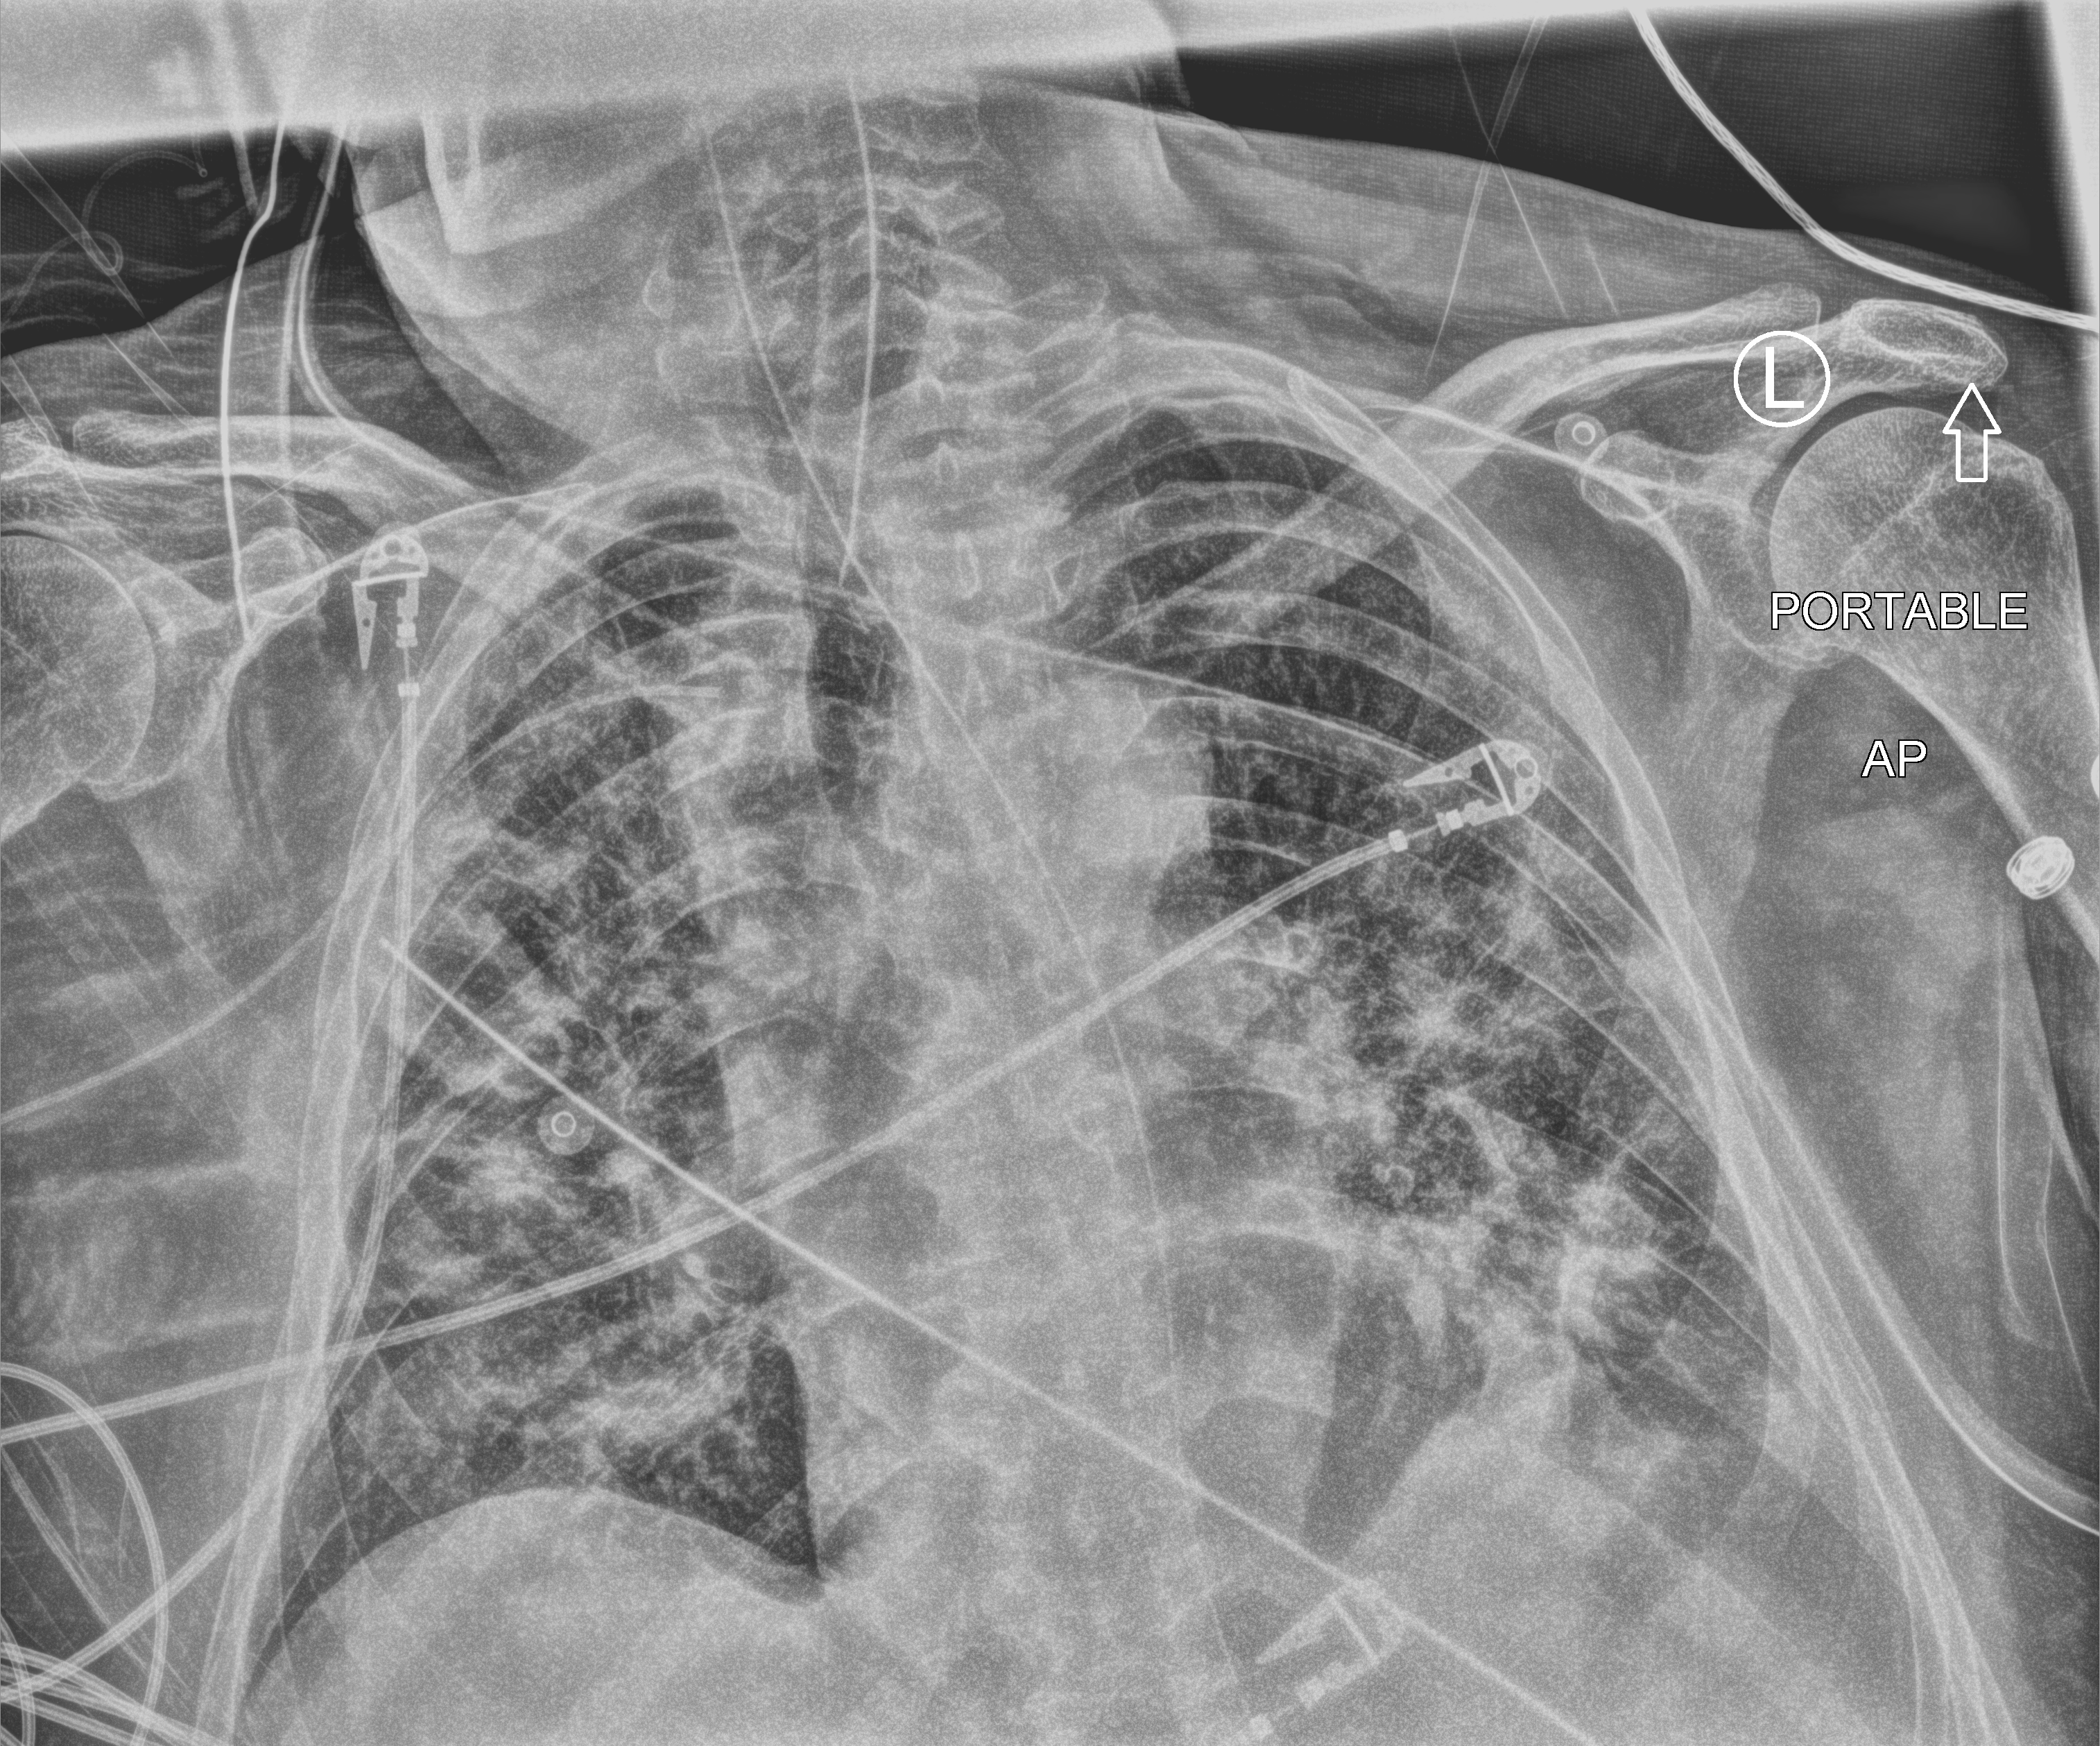
Portable chest radiograph. Patient hospitalised with COVID-19; male, aged 60–74 years.
Hospital-stay facts (about this admission, not read from this image; timing relative to this image not recorded): hypertension (admission record): no.